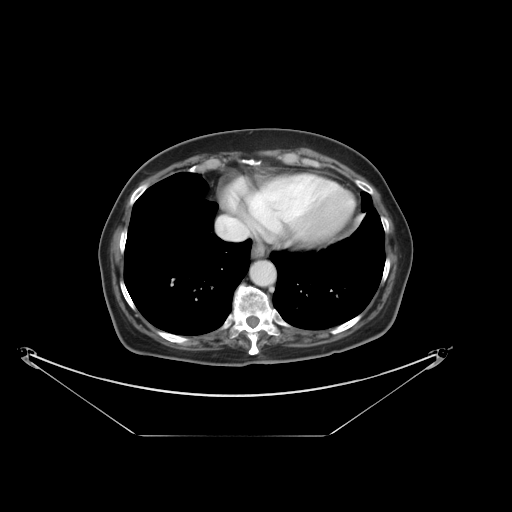
Contrast-enhanced abdominal CT, one axial slice; position 34 of 36 along the scan axis; intravenous contrast given; soft-tissue window (W 400 / L 40 HU); 512 × 512 image matrix, field of view 500 × 500 mm. Female patient, age 70 years. Case-level facts recorded for this patient, not image findings: diagnosis: colorectal cancer liver metastases, imaged before liver resection; multiple liver metastases: no; largest metastasis: 2.5 cm.
Structures marked on this image (expert manual segmentation):
- hepatic veins: box from (x=217, y=216) to (x=237, y=241) px